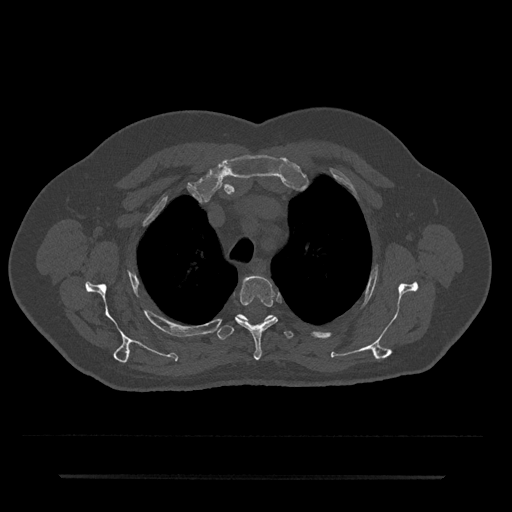
CT including the spine, one axial slice; slice 558 of 797 in the series (ordered by position); 120 kVp; bone window (W 1800 / L 400 HU); 0.5 mm slice thickness; 512 × 512 image matrix. Male patient, age 69 years. Case-level facts recorded for this patient, not image findings: primary cancer: prostate.
Annotated regions visible in this slice (semi-automatically segmented with operator editing):
- T3 vertebra: bounding box <235,275,278,360> (left, top, right, bottom; pixels)
- T4 vertebra: <217,314,293,340>